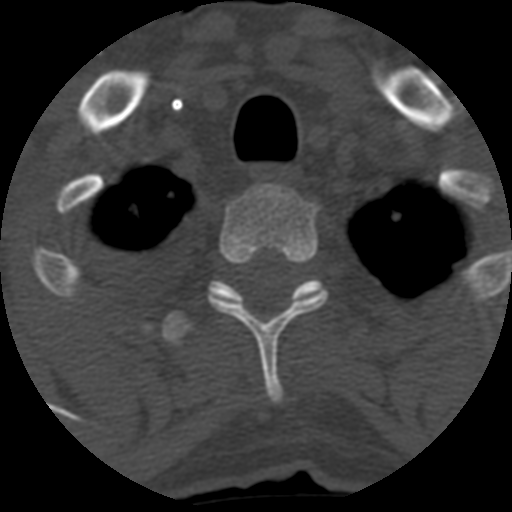
CT including the spine, one axial slice; slice 500 of 708 in the series (ordered by position); 120 kVp; one of 3 acquisitions stored at this slice position; bone window (W 1800 / L 400 HU); 512 × 512 image matrix, field of view 160 × 160 mm. Patient age 55 years. From the clinical record (not read from this slice): primary cancer: colon; vertebrae with lytic lesions (as recorded): T12, L1, L5.
Annotated regions visible in this slice (semi-automatically segmented with operator editing):
- T2 vertebra: bounding box (x1, y1, x2, y2) in pixels: (210, 183, 327, 404)
- T3 vertebra: (161, 280, 320, 345)